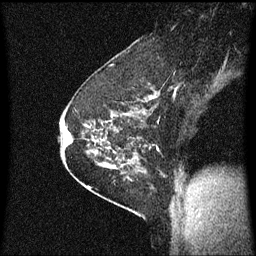
Breast MRI (dynamic contrast-enhanced), one sagittal slice; position 42 of 60 along the scan axis; dynamic contrast-enhanced series, image 2 of 3 at this slice position (ordered by acquisition); 1.5 T; TE 4.2 ms, TR 8.4 ms; 2 mm slice thickness; 256 × 256 image matrix, field of view 200 × 200 mm. Patient: female, 60 years.
Structures marked on this image (semi-automatic segmentation, software-assisted and operator-edited):
- analysis volume of interest (the breast-tissue region the enhancement analysis was run in; not a lesion): bounding box (x1, y1, x2, y2) in pixels: (69, 66, 146, 193)
- tumour enhancement mask (voxels above the 70 % enhancement threshold inside the analysis volume of interest): (87, 110, 145, 171)